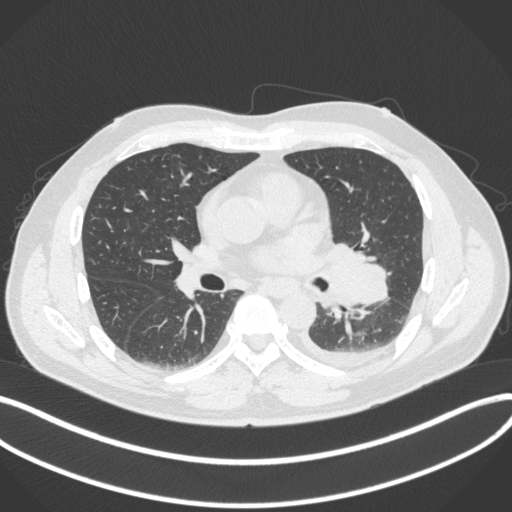
Chest CT, one axial slice; slice 191 of 350 in the series (ordered by position); reconstruction kernel B31f; lung window (W 1500 / L -600 HU); 1 mm slice thickness; 512 × 512 image matrix, field of view 400 × 400 mm. Male patient, age 58 years. From the clinical record (not read from this slice): clinical TNM (as recorded): T3 N1 M1b; histopathological grade: G3.
Structures marked on this image (rectangle marked by the reading radiologist):
- lung tumour (recorded histology: small cell carcinoma): bounding box (x1, y1, x2, y2) in pixels: (312, 238, 387, 314)